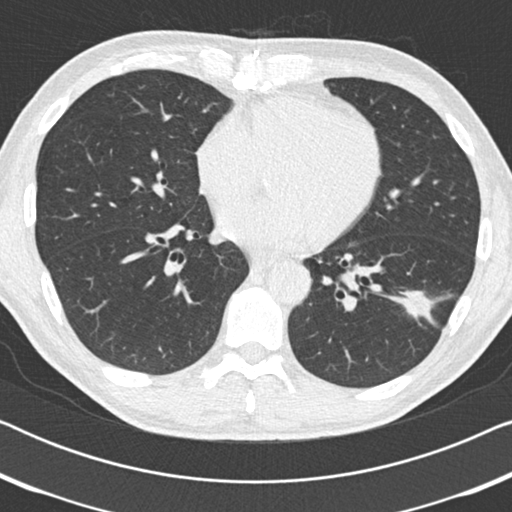
Low-dose screening chest CT, one axial slice; slice 79 of 186 in the series (ordered by position); 120 kVp; lung window (W 1500 / L -600 HU); 2 mm slice thickness; 512 × 512 image matrix.
Outlined on this slice (manually delineated by an expert):
- lesion 1 (tumor, lower lobe of left lung): bounding box [x1, y1, x2, y2] px = [401, 292, 433, 317]